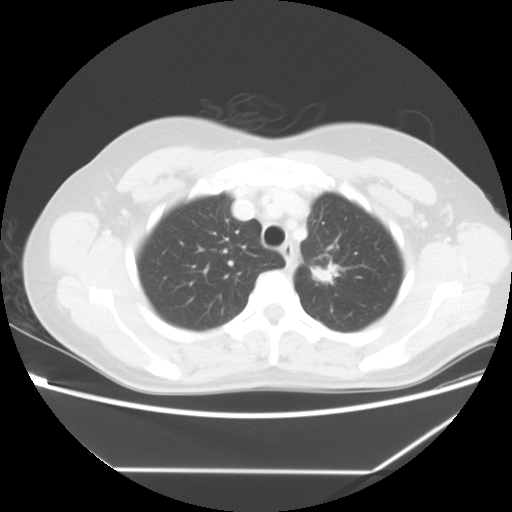
Chest CT, one axial slice; slice 47 of 60 in the series (ordered by position); reconstruction kernel STANDARD; 140 kVp; lung window (W 1500 / L -600 HU); 512 × 512 image matrix. Female patient, age 43 years. Case-level facts recorded for this patient, not image findings: clinical TNM (as recorded): T1c N0 M1b.
Structures marked on this image (rectangle marked by the reading radiologist):
- lung tumour (recorded histology: adenocarcinoma): bounding box (x1, y1, x2, y2) in pixels: (301, 256, 342, 288)